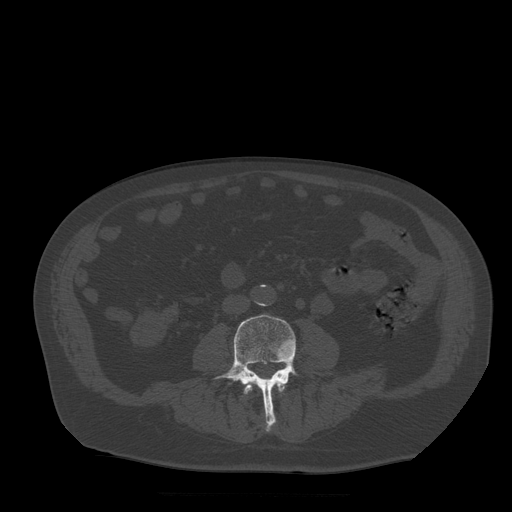
CT including the spine, one axial slice; slice 116 of 522 in the series (ordered by position); bone window (W 1800 / L 400 HU); 1.25 mm slice thickness; 512 × 512 image matrix, field of view 420 × 420 mm. Patient age 72 years. From the clinical record (not read from this slice): primary cancer: prostate.
Outlined on this slice (semi-automatic segmentation, software-assisted and operator-edited):
- L3 vertebra: bounding box (x1, y1, x2, y2) in pixels: (244, 380, 285, 395)
- L4 vertebra: (214, 315, 299, 431)
- L5 vertebra: (280, 363, 294, 371)